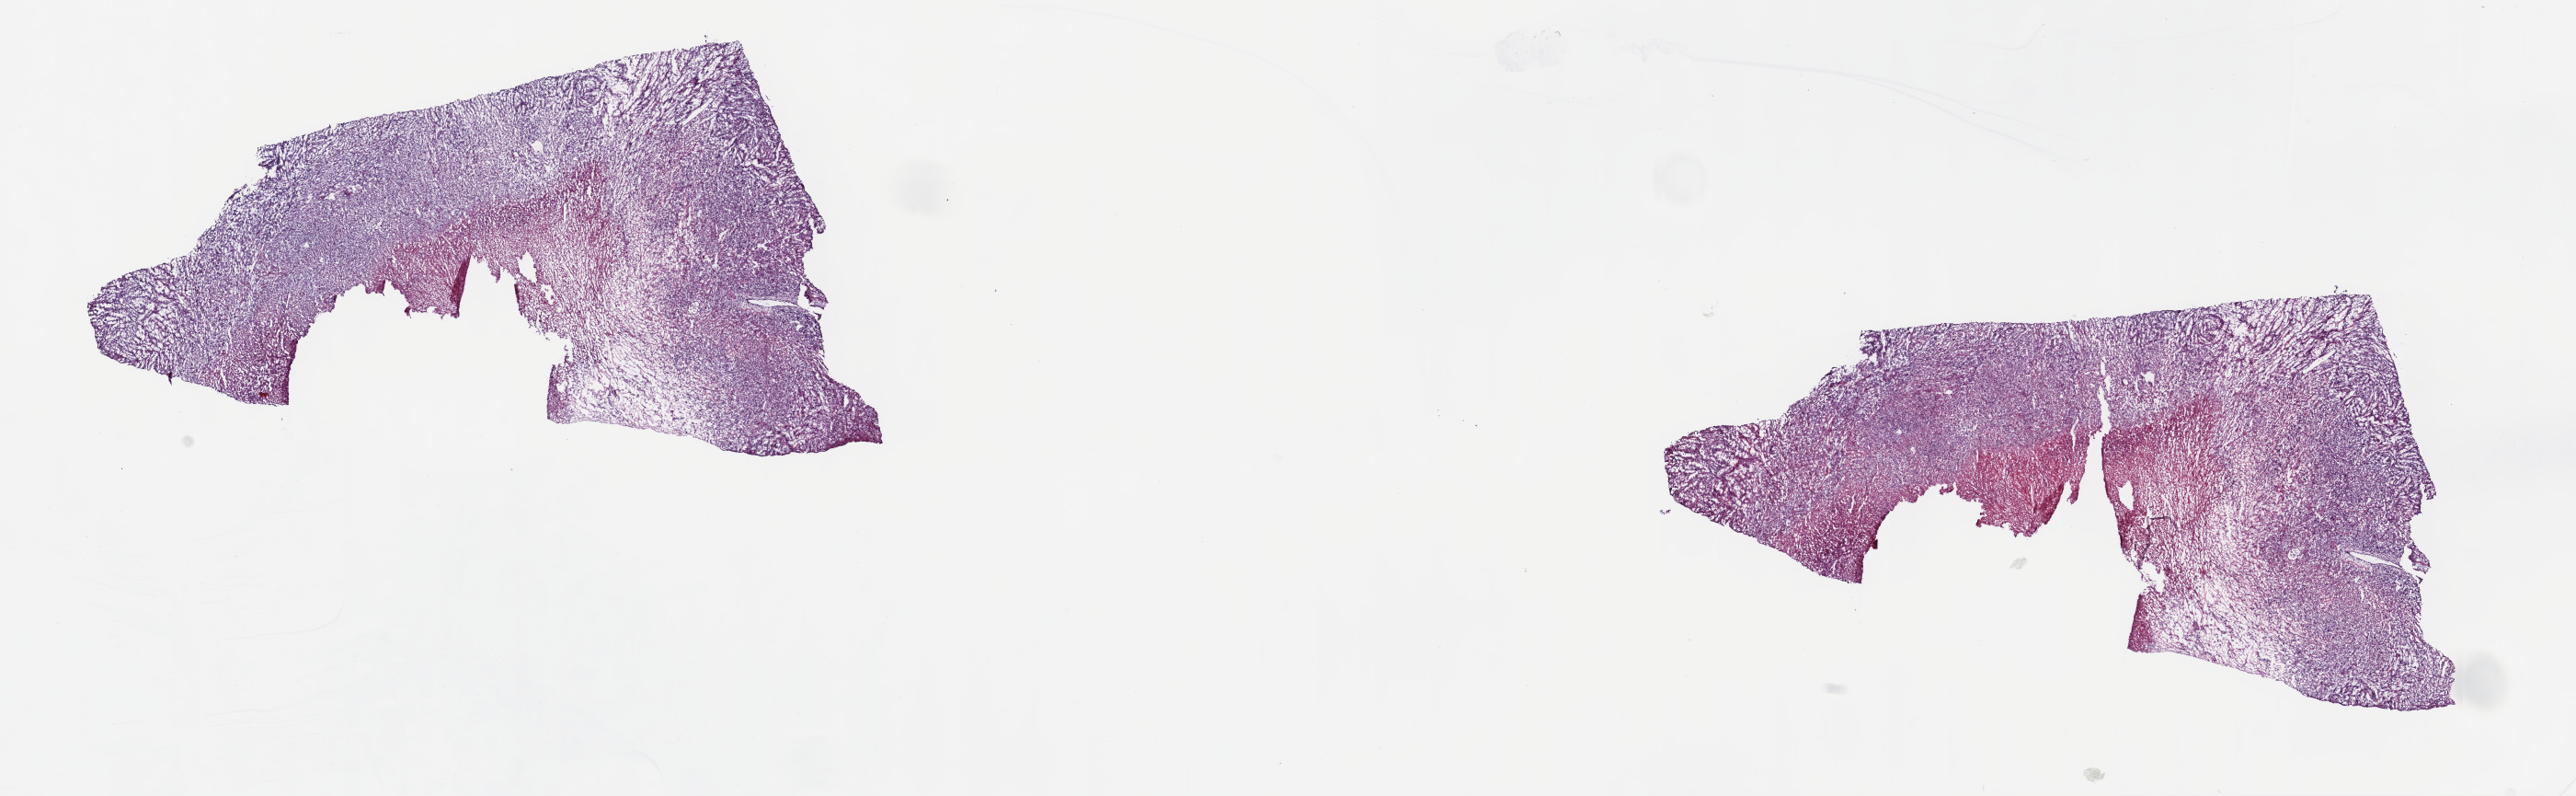
H&E whole-slide image, a low-resolution overview of the entire scanned area, about 22.7 x 7.0 mm, frozen section from the top of the tissue portion, sample: primary tumour, mesothelium. Patient: male, age at initial diagnosis 61 years. Composition of this section per pathologist review: tumour cells 70%, tumour nuclei 70%, normal cells 0%, stromal cells 20%, necrosis 10%. Inflammatory infiltration, as recorded: lymphocyte infiltration 60%, monocyte infiltration 10%, neutrophil infiltration 10%.
AJCC pathologic stage: IV. Laterality: right. Histologic diagnosis: Mesothelioma, biphasic, malignant (pleura, NOS).